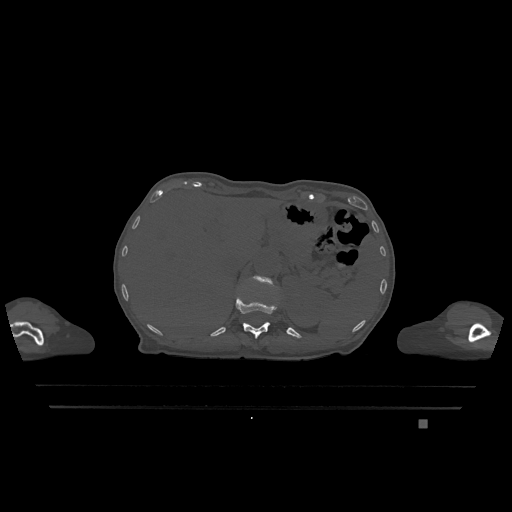
CT including the spine, one axial slice. Slice 524 of 1317 in the series (ordered by position). Bone window (W 1800 / L 400 HU). 0.5 mm slice thickness. 512 × 512 image matrix, field of view 500 × 500 mm. Patient: female, 74 years. From the clinical record (not read from this slice): primary cancer: lung; vertebrae with lytic lesions (as recorded): T1, T4, T5, T6, L4, L5.
Annotated regions visible in this slice (semi-automatically segmented with operator editing):
- L1 vertebra: bounding box <253,276,273,287> (left, top, right, bottom; pixels)
- T12 vertebra: <236,296,277,339>